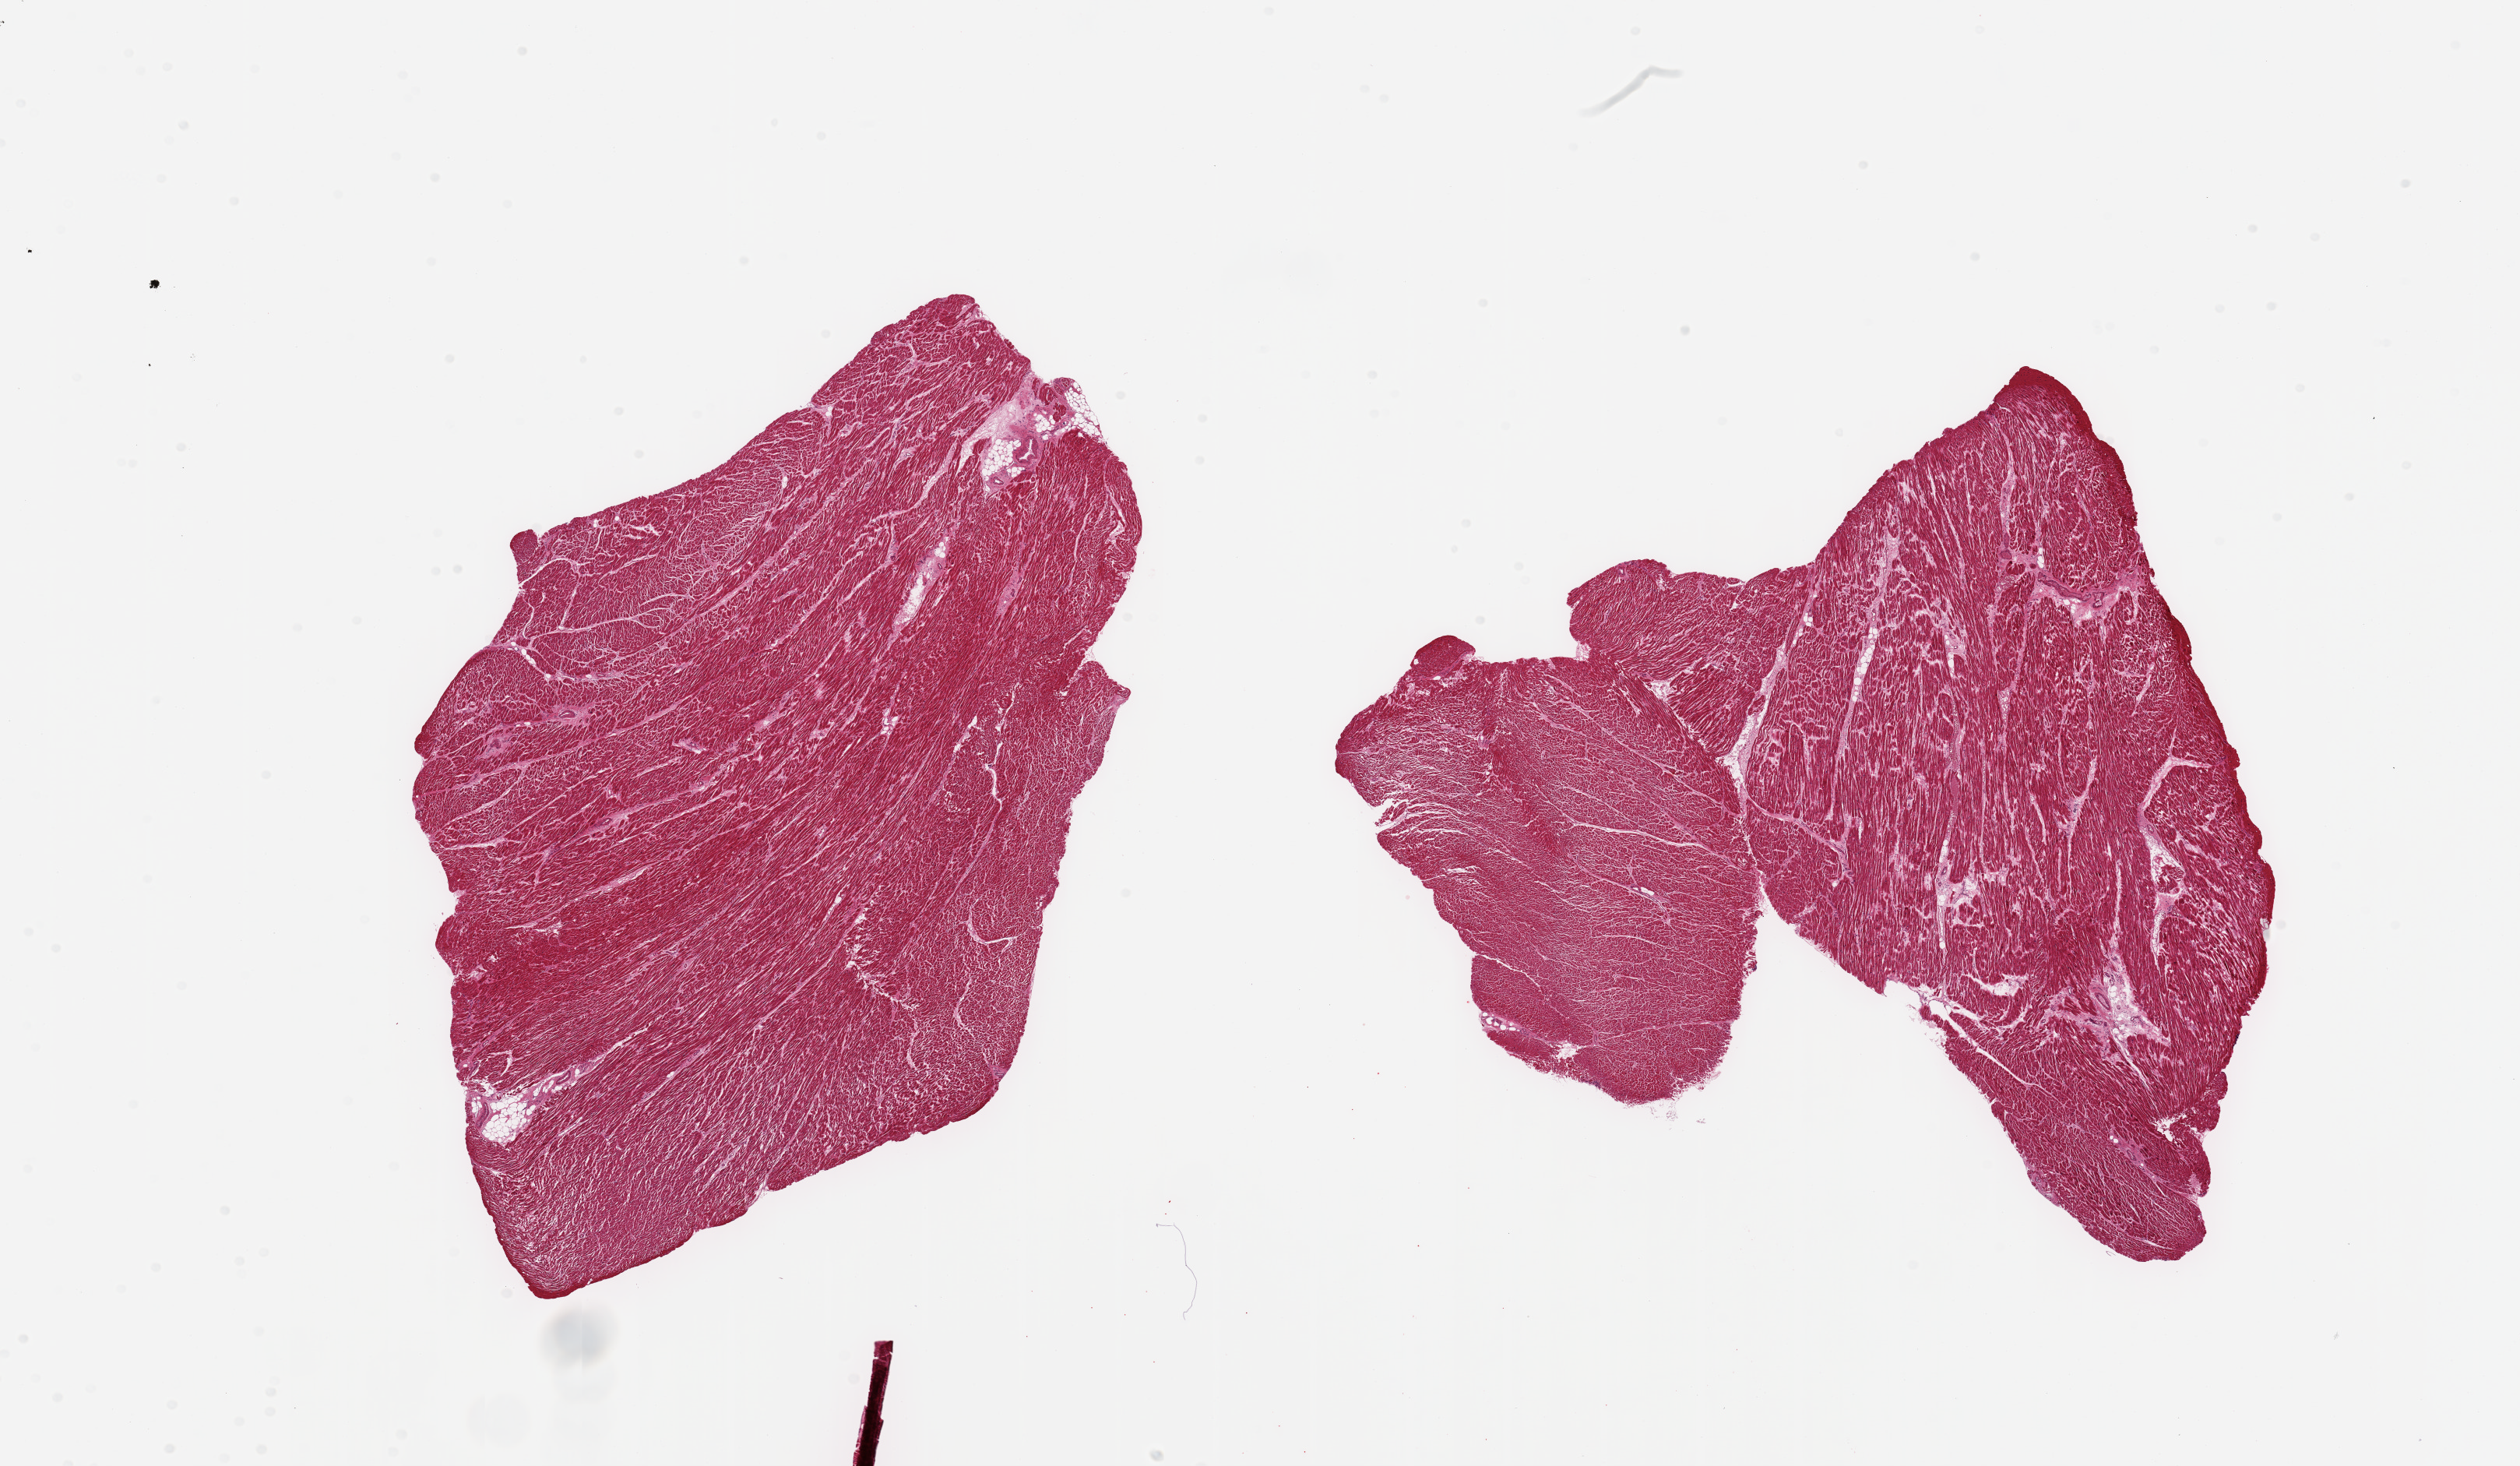
Digitized haematoxylin and eosin-stained section — shown as a low-resolution overview of the whole scanned area (about 25.6 x 14.9 mm, acquisition: 20x scan); PAXgene-fixed, paraffin-embedded tissue; section of heart (target tissue); donor tissue sample. Donor: male.
Review note (as recorded): 2 pieces; patchy hypereosinophilia; no scars.